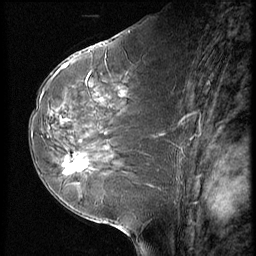
Breast MRI (dynamic contrast-enhanced), one sagittal slice. Position 31 of 56 along the scan axis. Dynamic contrast-enhanced series, image 2 of 3 at this slice position (ordered by acquisition). 1.5 T. TE 4.2 ms, TR 9 ms. 2.5 mm slice thickness. 256 × 256 image matrix, field of view 180 × 180 mm. Female patient, age 58 years. Case-level facts recorded for this patient, not image findings: setting: breast cancer imaged before/during neoadjuvant chemotherapy; receptor status: HR-positive, HER2-negative.
Structures marked on this image (semi-automatically segmented with operator editing):
- analysis volume of interest (the breast-tissue region the enhancement analysis was run in; not a lesion): bounding box (x1, y1, x2, y2) in pixels: (56, 146, 99, 182)
- tumour enhancement mask (voxels above the 140 % enhancement threshold inside the analysis volume of interest): (63, 153, 88, 173)